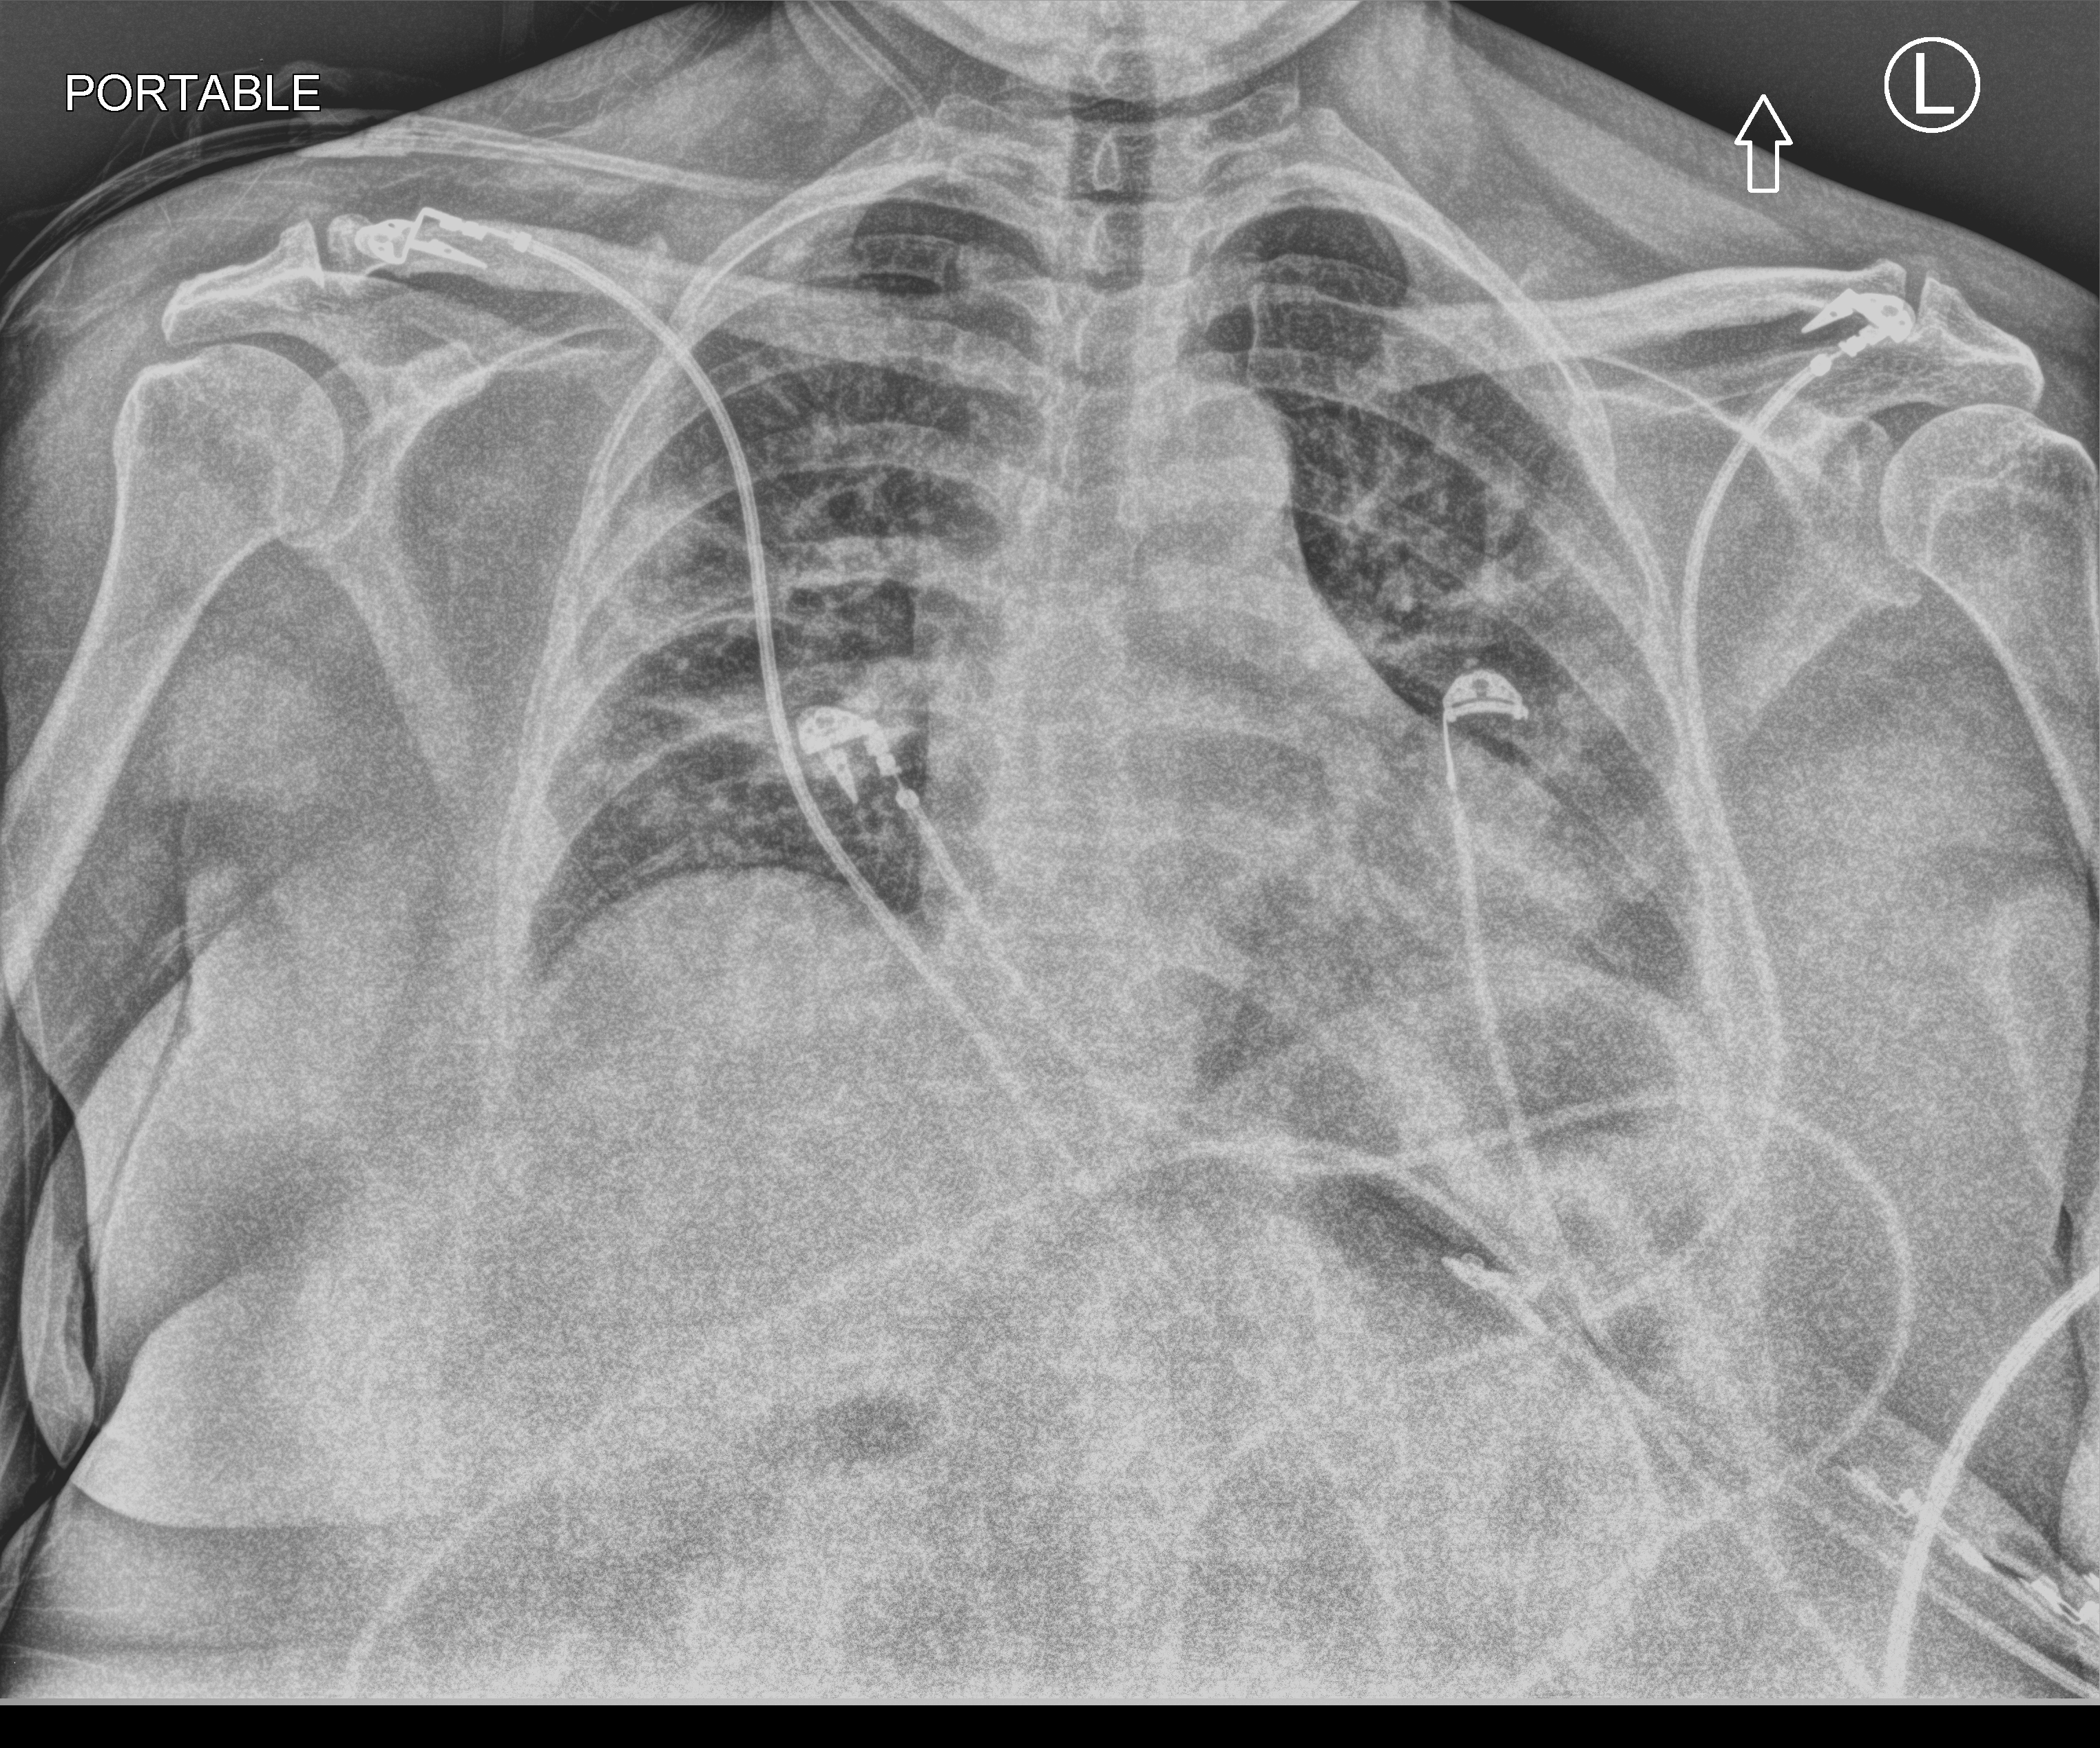
Chest X-ray (portable). Patient hospitalised with COVID-19; female, aged 18–59 years.
Admission-level facts for this patient (not findings on this image; timing relative to this image not recorded): hypertension (admission record): no; admitted to intensive care during this hospital stay: no; mechanically ventilated during this hospital stay: no.